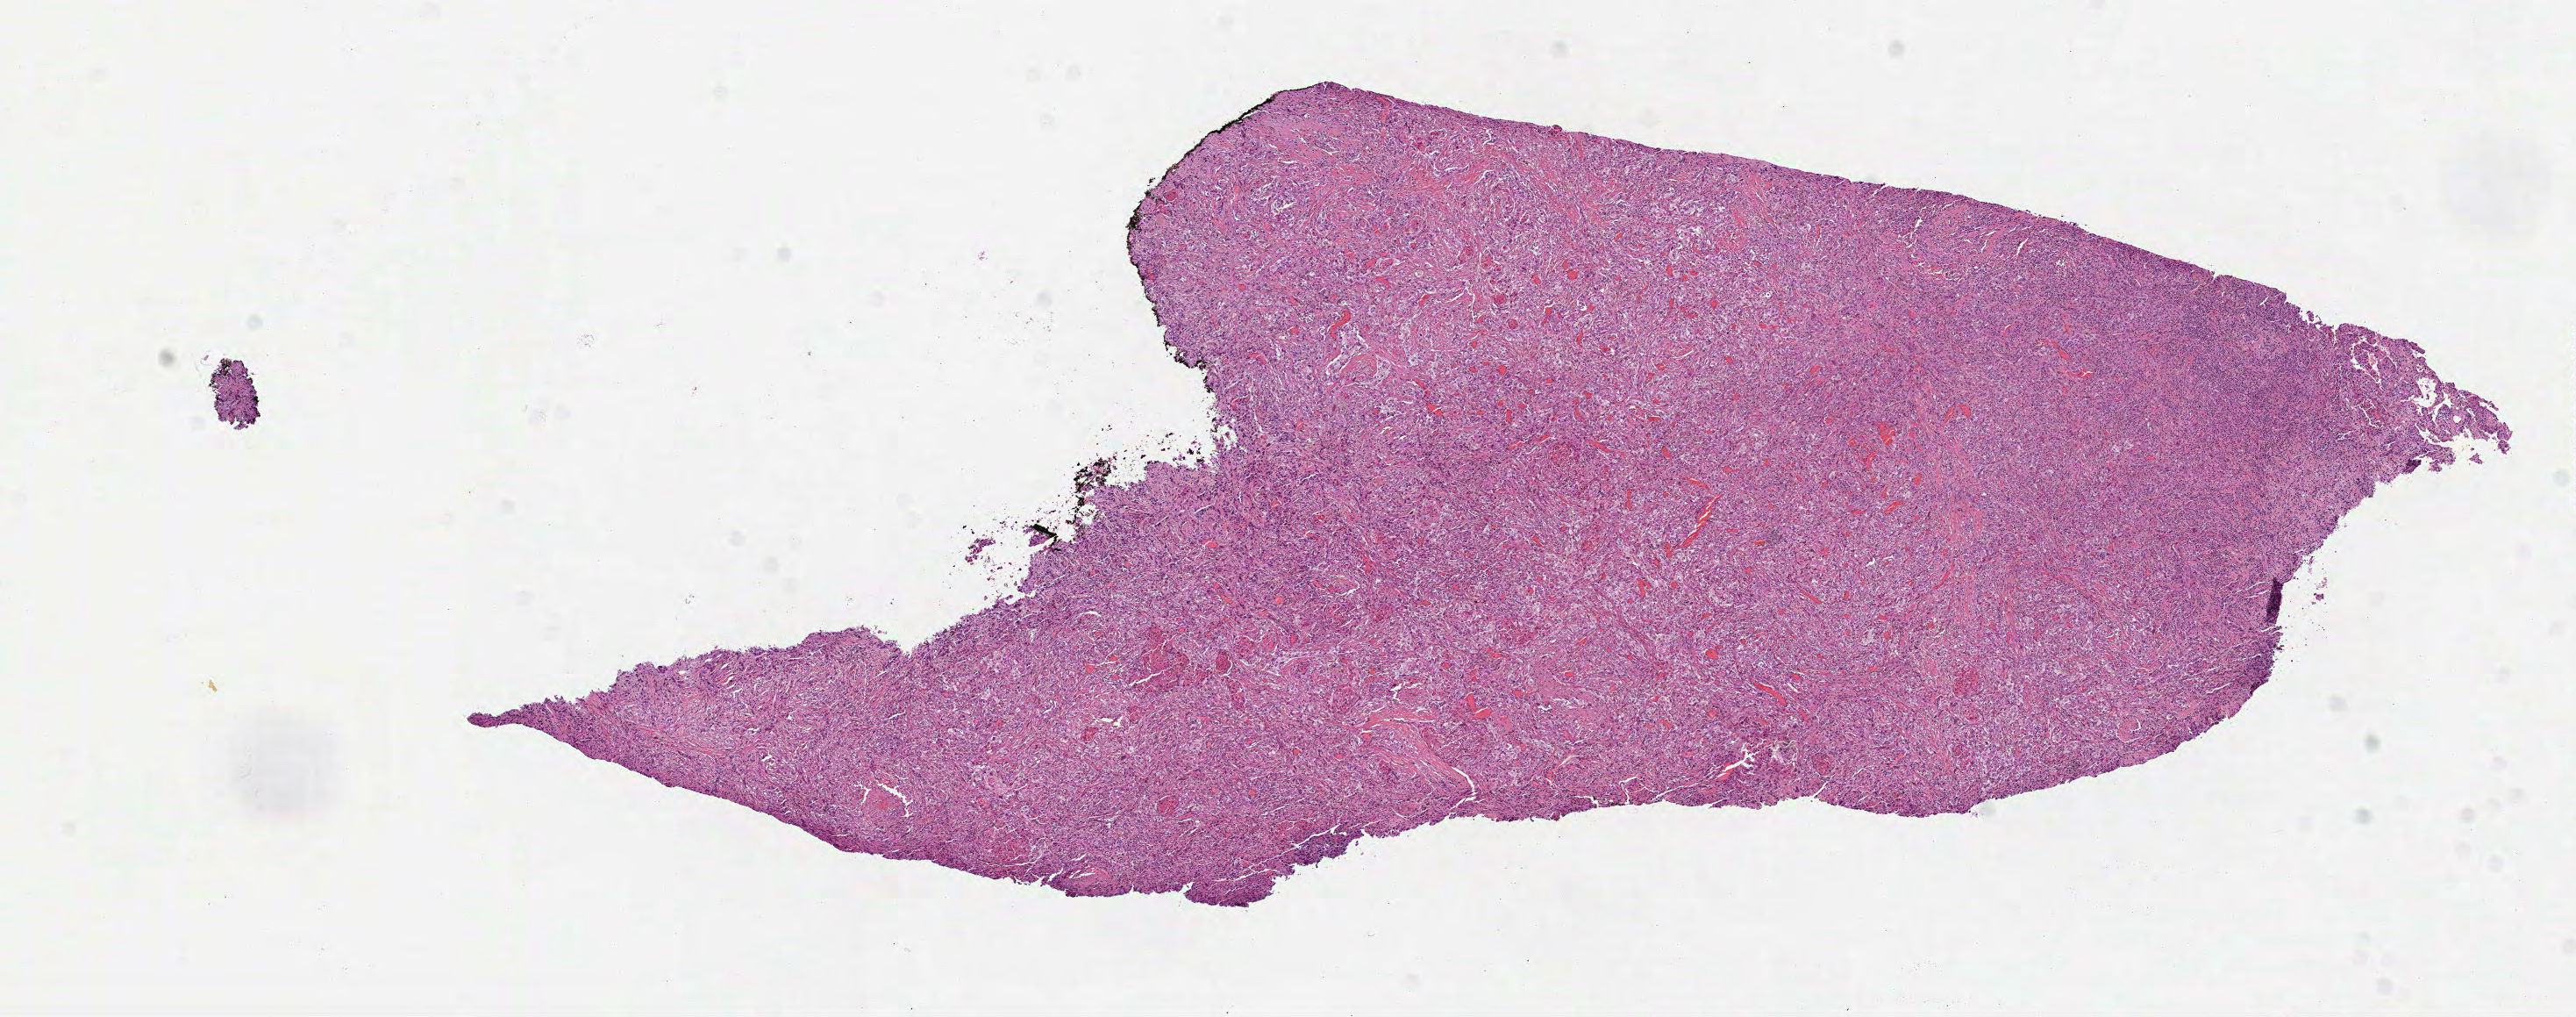
Digitized H&E tissue section (whole slide), whole scanned area (about 11.8 x 4.7 mm, from a 40x scan) shown as a low-resolution overview; FFPE section; lung, primary tumour sample. Patient: male, age at initial diagnosis 74 years.
• histologic diagnosis: Squamous cell carcinoma, NOS (upper lobe, lung)
• laterality: right
• TNM: T3 N0 MX
• AJCC pathologic stage: IIB (7th edition)